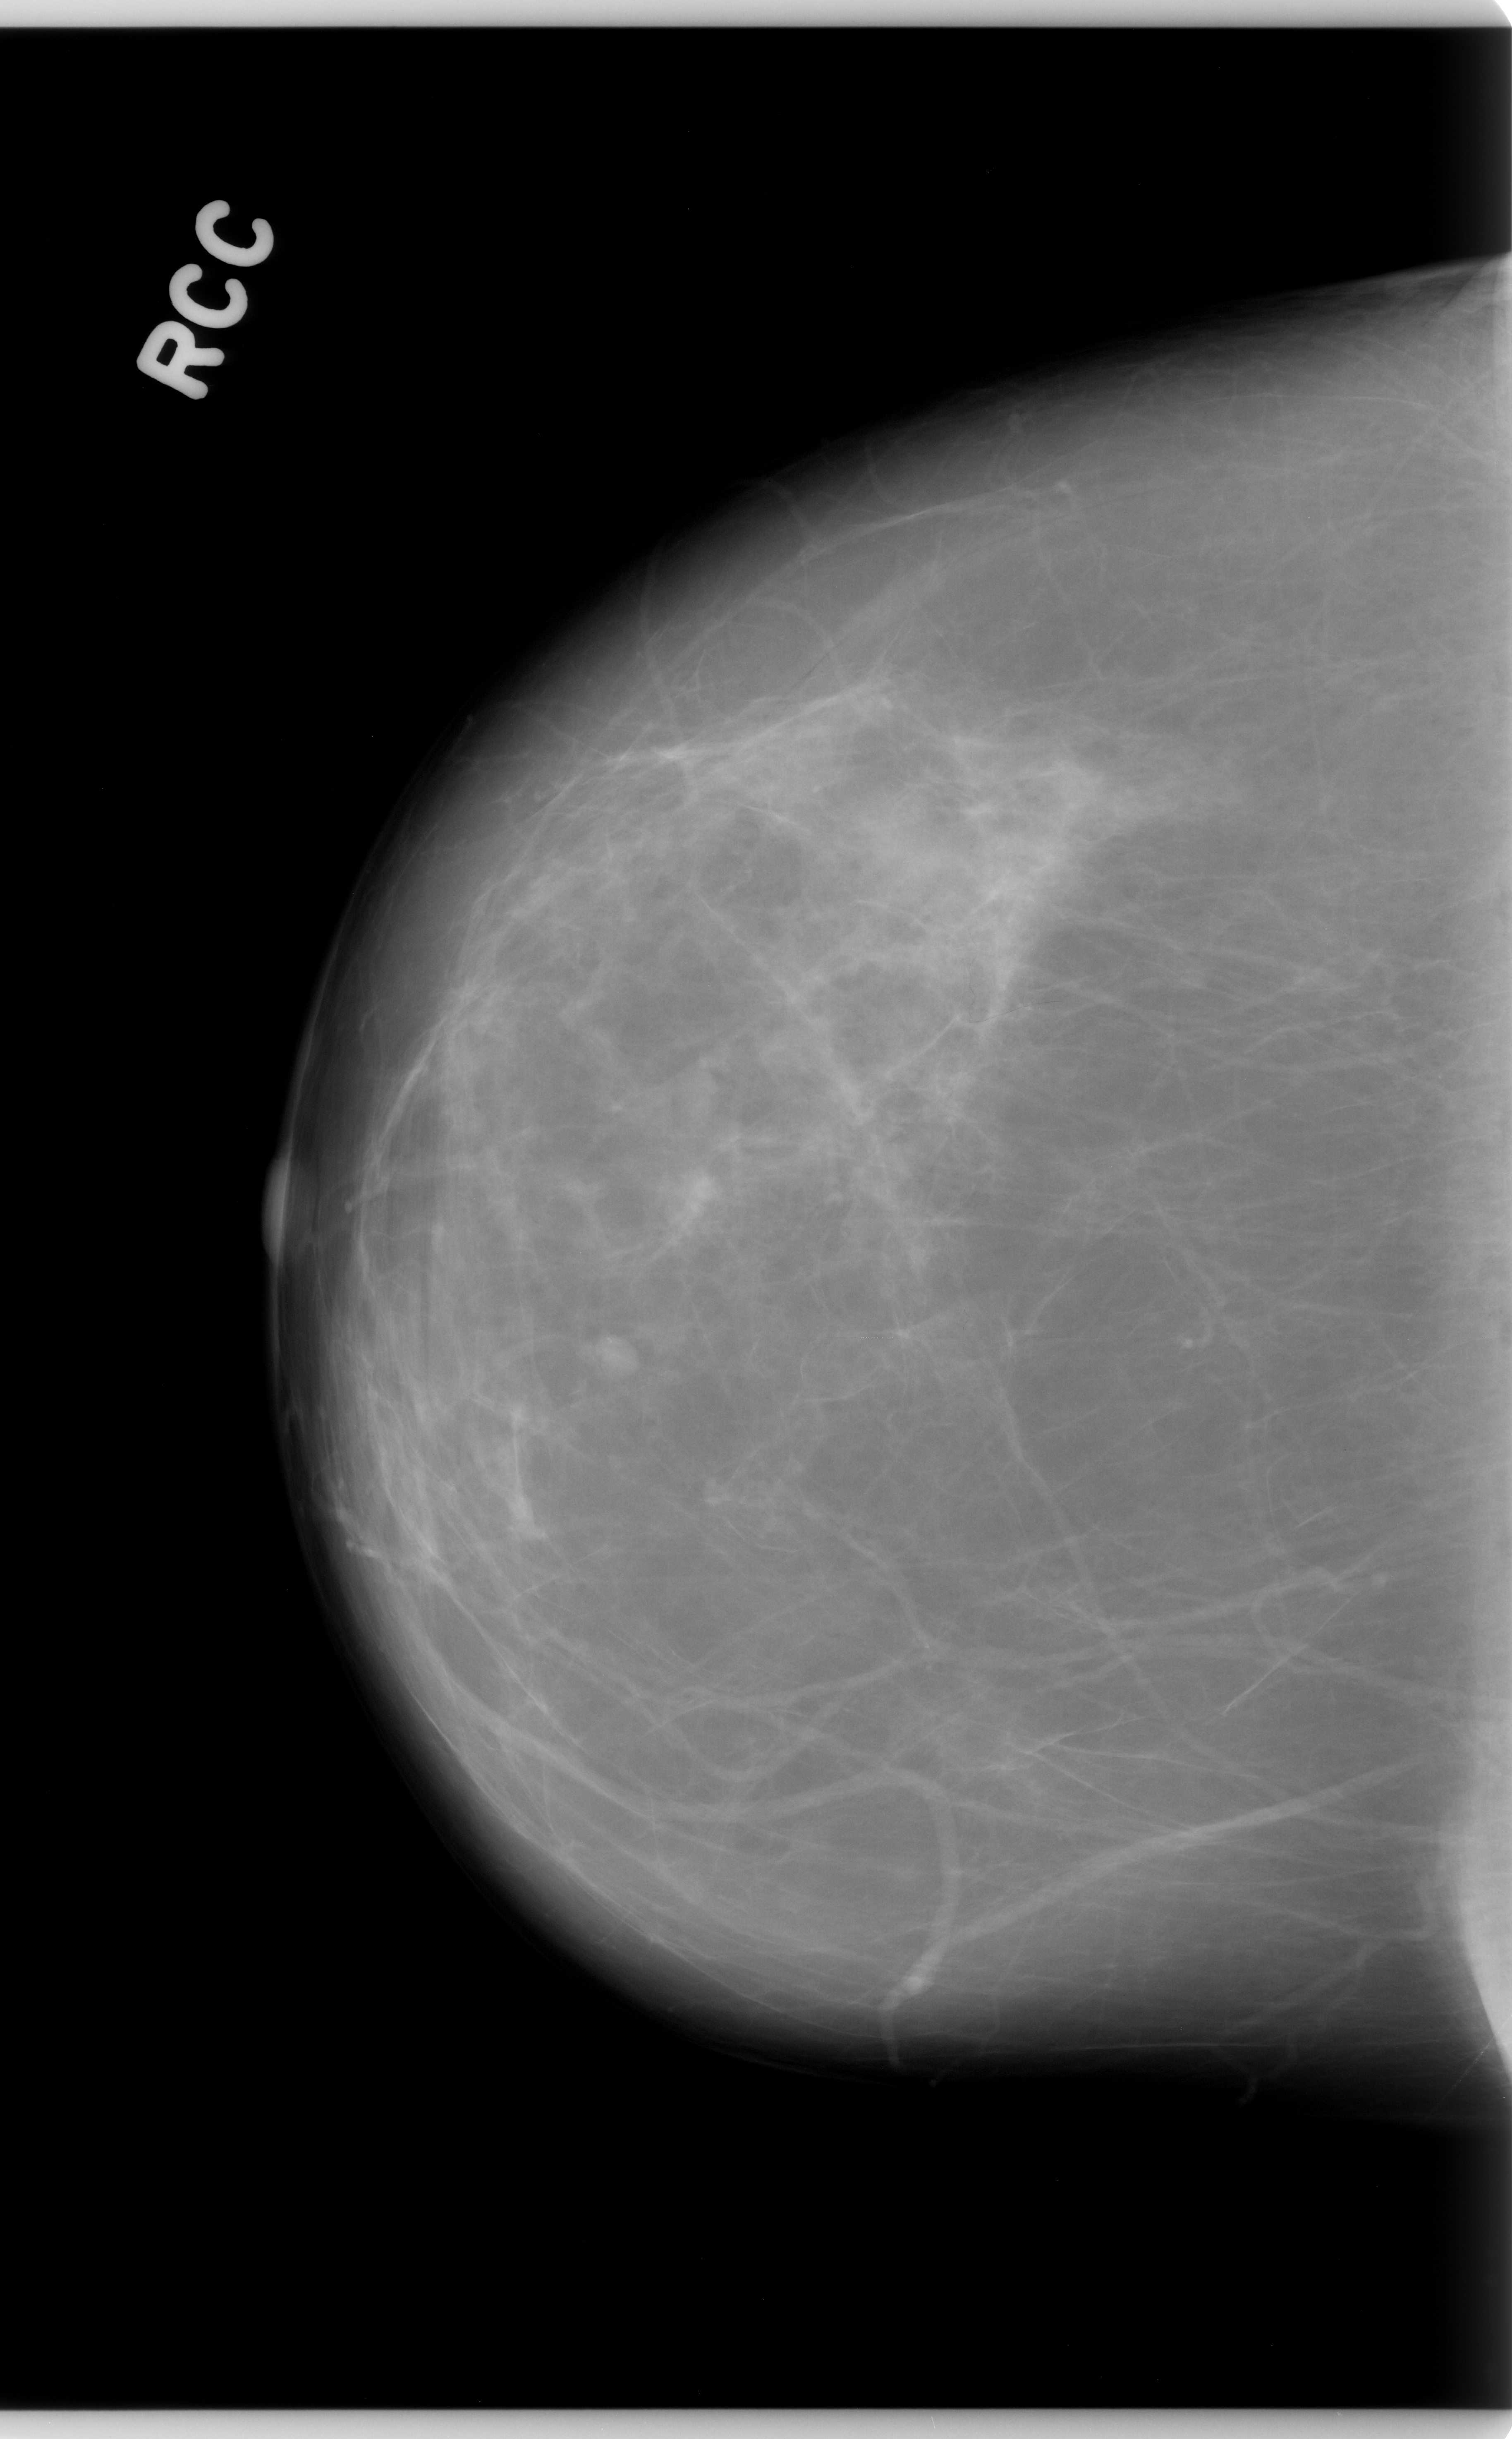
Digitized screen-film mammogram. Right breast. Craniocaudal (CC) view. BI-RADS breast density category 1 (scale 1–4). 1512 × 2439 image matrix.
Expert-marked regions of interest on this film, with their recorded descriptors:
- calcifications, morphology punctate, distribution clustered; BI-RADS assessment category 4; subtlety rating 5 on a 1 (subtle) to 5 (obvious) scale; pathology (as recorded): benign: bounding box [x1, y1, x2, y2] px = [552, 1290, 659, 1424]